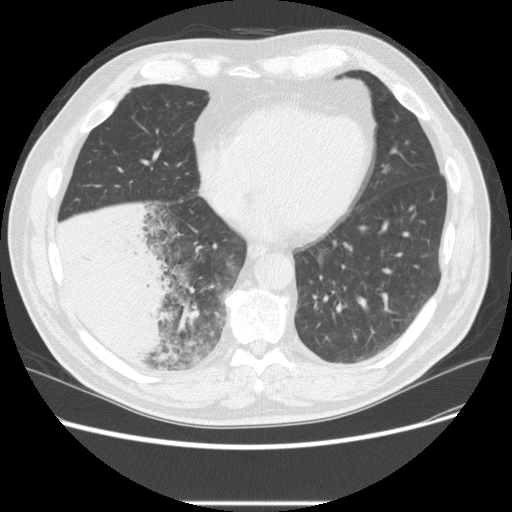
Low-dose screening chest CT, one axial slice; slice 79 of 233 in the series (ordered by position); 120 kVp; lung window (W 1500 / L -600 HU); 2.5 mm slice thickness; 512 × 512 image matrix, field of view 380 × 380 mm.
Annotated regions visible in this slice (expert manual segmentation):
- lesion 3 (tumor, lower lobe of right lung): bounding box <54,204,175,366> (left, top, right, bottom; pixels)